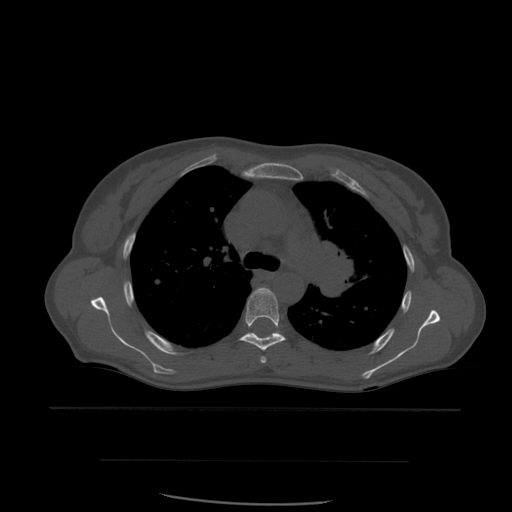
CT including the spine, one axial slice. Position 411 of 574 along the scan axis. Bone window (W 1800 / L 400 HU). 1.25 mm slice thickness. 512 × 512 image matrix. Patient age 48 years. From the clinical record (not read from this slice): primary cancer: lung; vertebrae with lytic lesions (as recorded): T11.
Outlined on this slice (semi-automatic segmentation, software-assisted and operator-edited):
- T4 vertebra: bounding box [x1, y1, x2, y2] px = [260, 357, 267, 363]
- T5 vertebra: [240, 287, 286, 351]